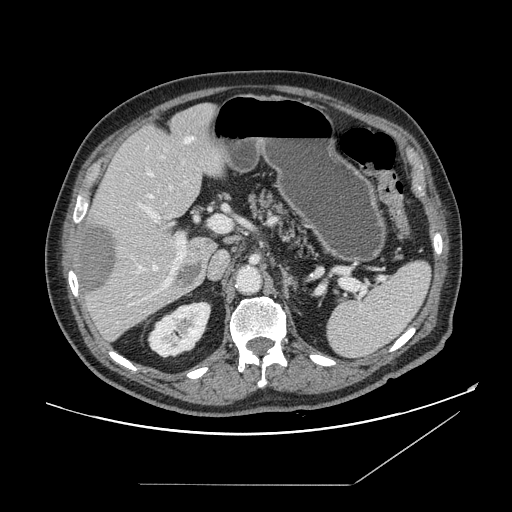
Contrast-enhanced abdominal CT, one axial slice; slice 94 of 166 in the series (ordered by position); 120 kVp; intravenous contrast given; soft-tissue window (W 400 / L 40 HU); 2.5 mm slice thickness; 512 × 512 image matrix. Male patient, age 80 years. Case-level facts recorded for this patient, not image findings: diagnosis: colorectal cancer liver metastases, imaged before liver resection.
Annotated regions visible in this slice (expert manual segmentation):
- hepatic veins: bounding box (x1, y1, x2, y2) in pixels: (140, 170, 172, 271)
- liver: (76, 104, 228, 341)
- planned liver remnant (the part of the liver to remain after resection): (95, 104, 227, 253)
- portal vein (with intrahepatic branches): (139, 204, 231, 288)
- liver metastasis: (79, 224, 202, 295)